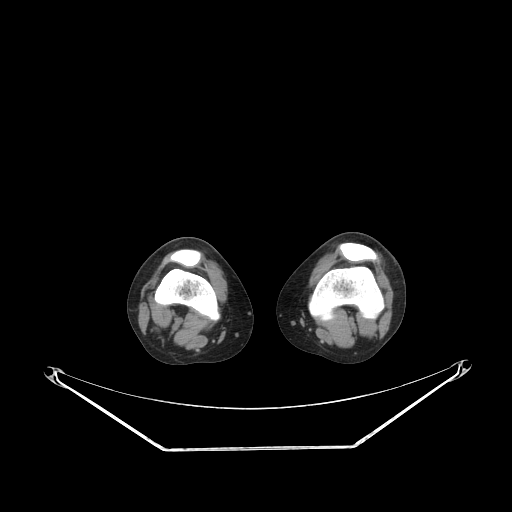
CT of an extremity soft-tissue mass (from a PET/CT study), one axial slice; slice 166 of 223 in the series (ordered by position); 140 kVp; soft-tissue window (W 400 / L 40 HU); 512 × 512 image matrix, field of view 500 × 500 mm. Female patient. Case-level facts recorded for this patient, not image findings: histological type: spindle cell suggestive of biphasic synovial sarcoma; grade: intermediate; site of the primary tumour: left knee.
Outlined on this slice (expert contour drawn on MRI and transferred to this co-registered scan by the dataset authors):
- gross tumour volume including surrounding oedema: bounding box <377,274,391,303> (left, top, right, bottom; pixels)
- gross tumour volume (mass): <377,274,391,302>